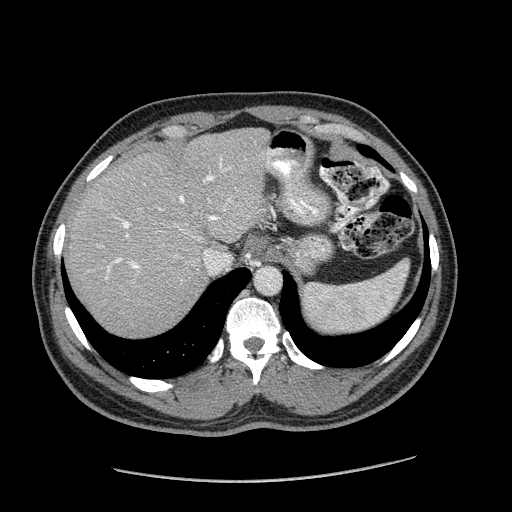
Contrast-enhanced abdominal CT (liver protocol), one axial slice; position 141 of 182 along the scan axis; reconstruction kernel STANDARD; 120 kVp; soft-tissue window (W 400 / L 40 HU); 2.5 mm slice thickness; 512 × 512 image matrix, field of view 400 × 400 mm. Case-level facts recorded for this patient, not image findings: diagnosis: hepatocellular carcinoma (patient treated with transarterial chemoembolisation; whether this scan precedes or follows treatment is not stated here); TNM stage (as recorded): Stage-I; Child-Pugh class: A; tumour differentiation: well differentiated; tumour size: 3.1 cm.
Annotated regions visible in this slice (semi-automatically segmented with operator editing):
- liver parenchyma outside the tumour (the mass and vessels are separate outlines, so this box may not span the whole liver): bounding box (x1, y1, x2, y2) in pixels: (66, 128, 268, 336)
- liver vessels: (105, 163, 231, 280)